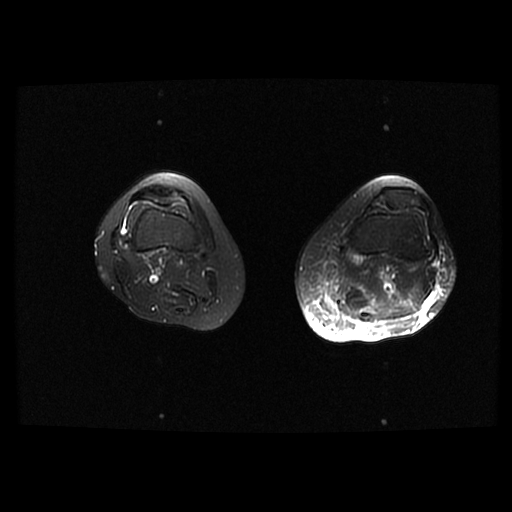
MRI of an extremity soft-tissue mass, one axial slice; slice 12 of 42 in the series (ordered by position); T2-weighted fat-saturated; 6 mm slice thickness; 512 × 512 image matrix. Female patient. Case-level facts recorded for this patient, not image findings: histological type: pleomorphic leiomyosarcoma; grade: high; site of the primary tumour: left thigh.
Structures marked on this image (outlined manually by an expert reader):
- gross tumour volume including surrounding oedema: bounding box <323,263,342,305> (left, top, right, bottom; pixels)